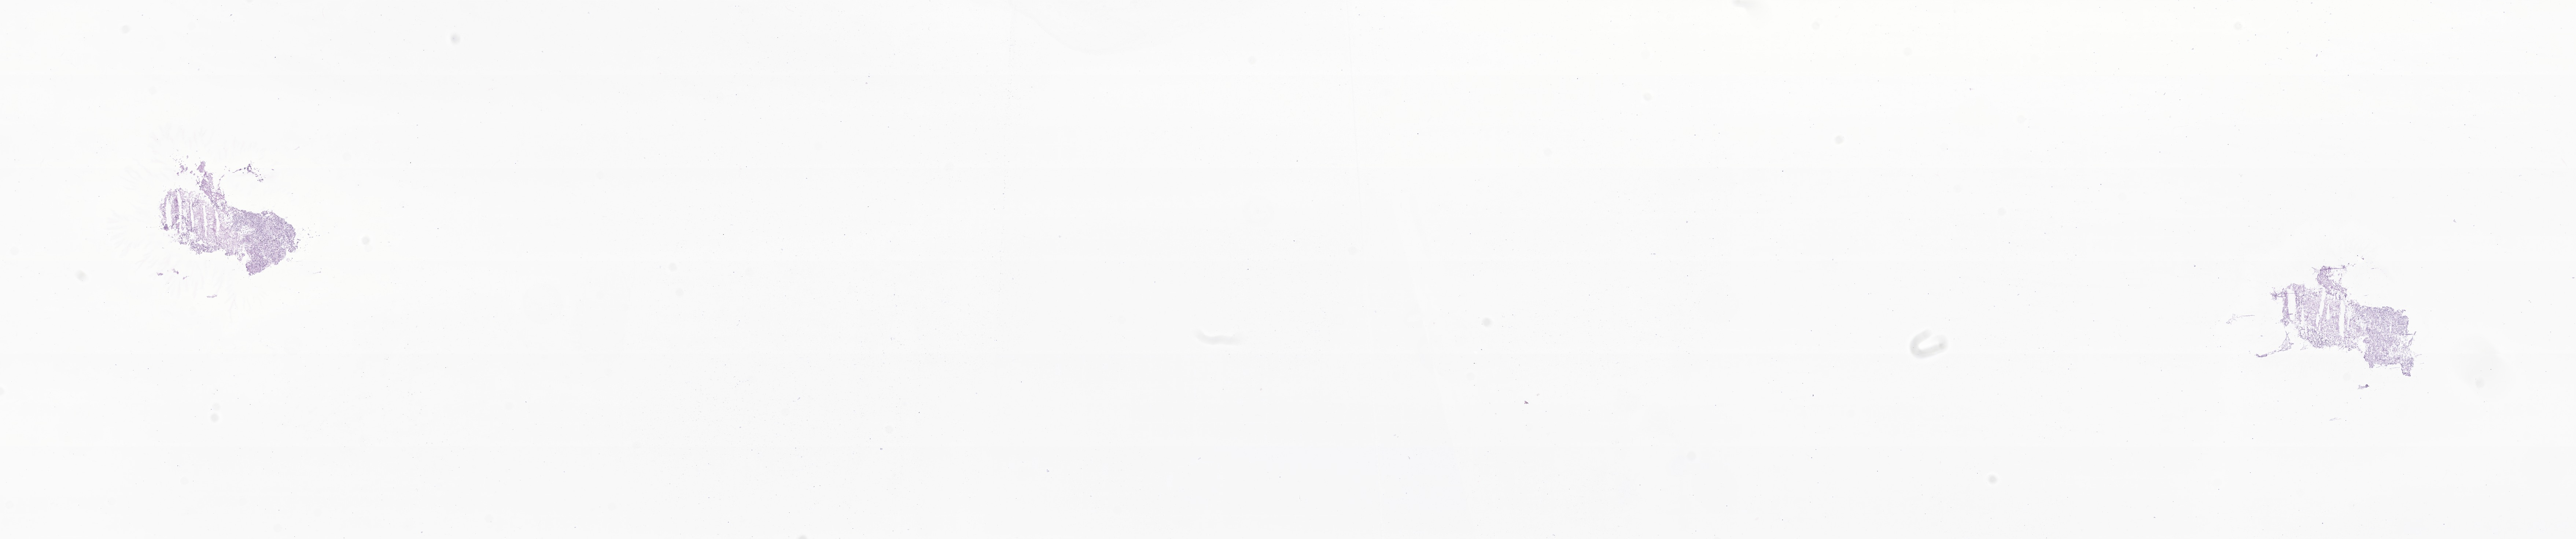
Digitized H&E-stained section of tumor tissue from the brain, low-resolution overview of the scanned area, about 29.6 x 6.2 mm, frozen section. Female patient, age 160 months (13 years 4 months).
* diagnosis: Glioma, malignant